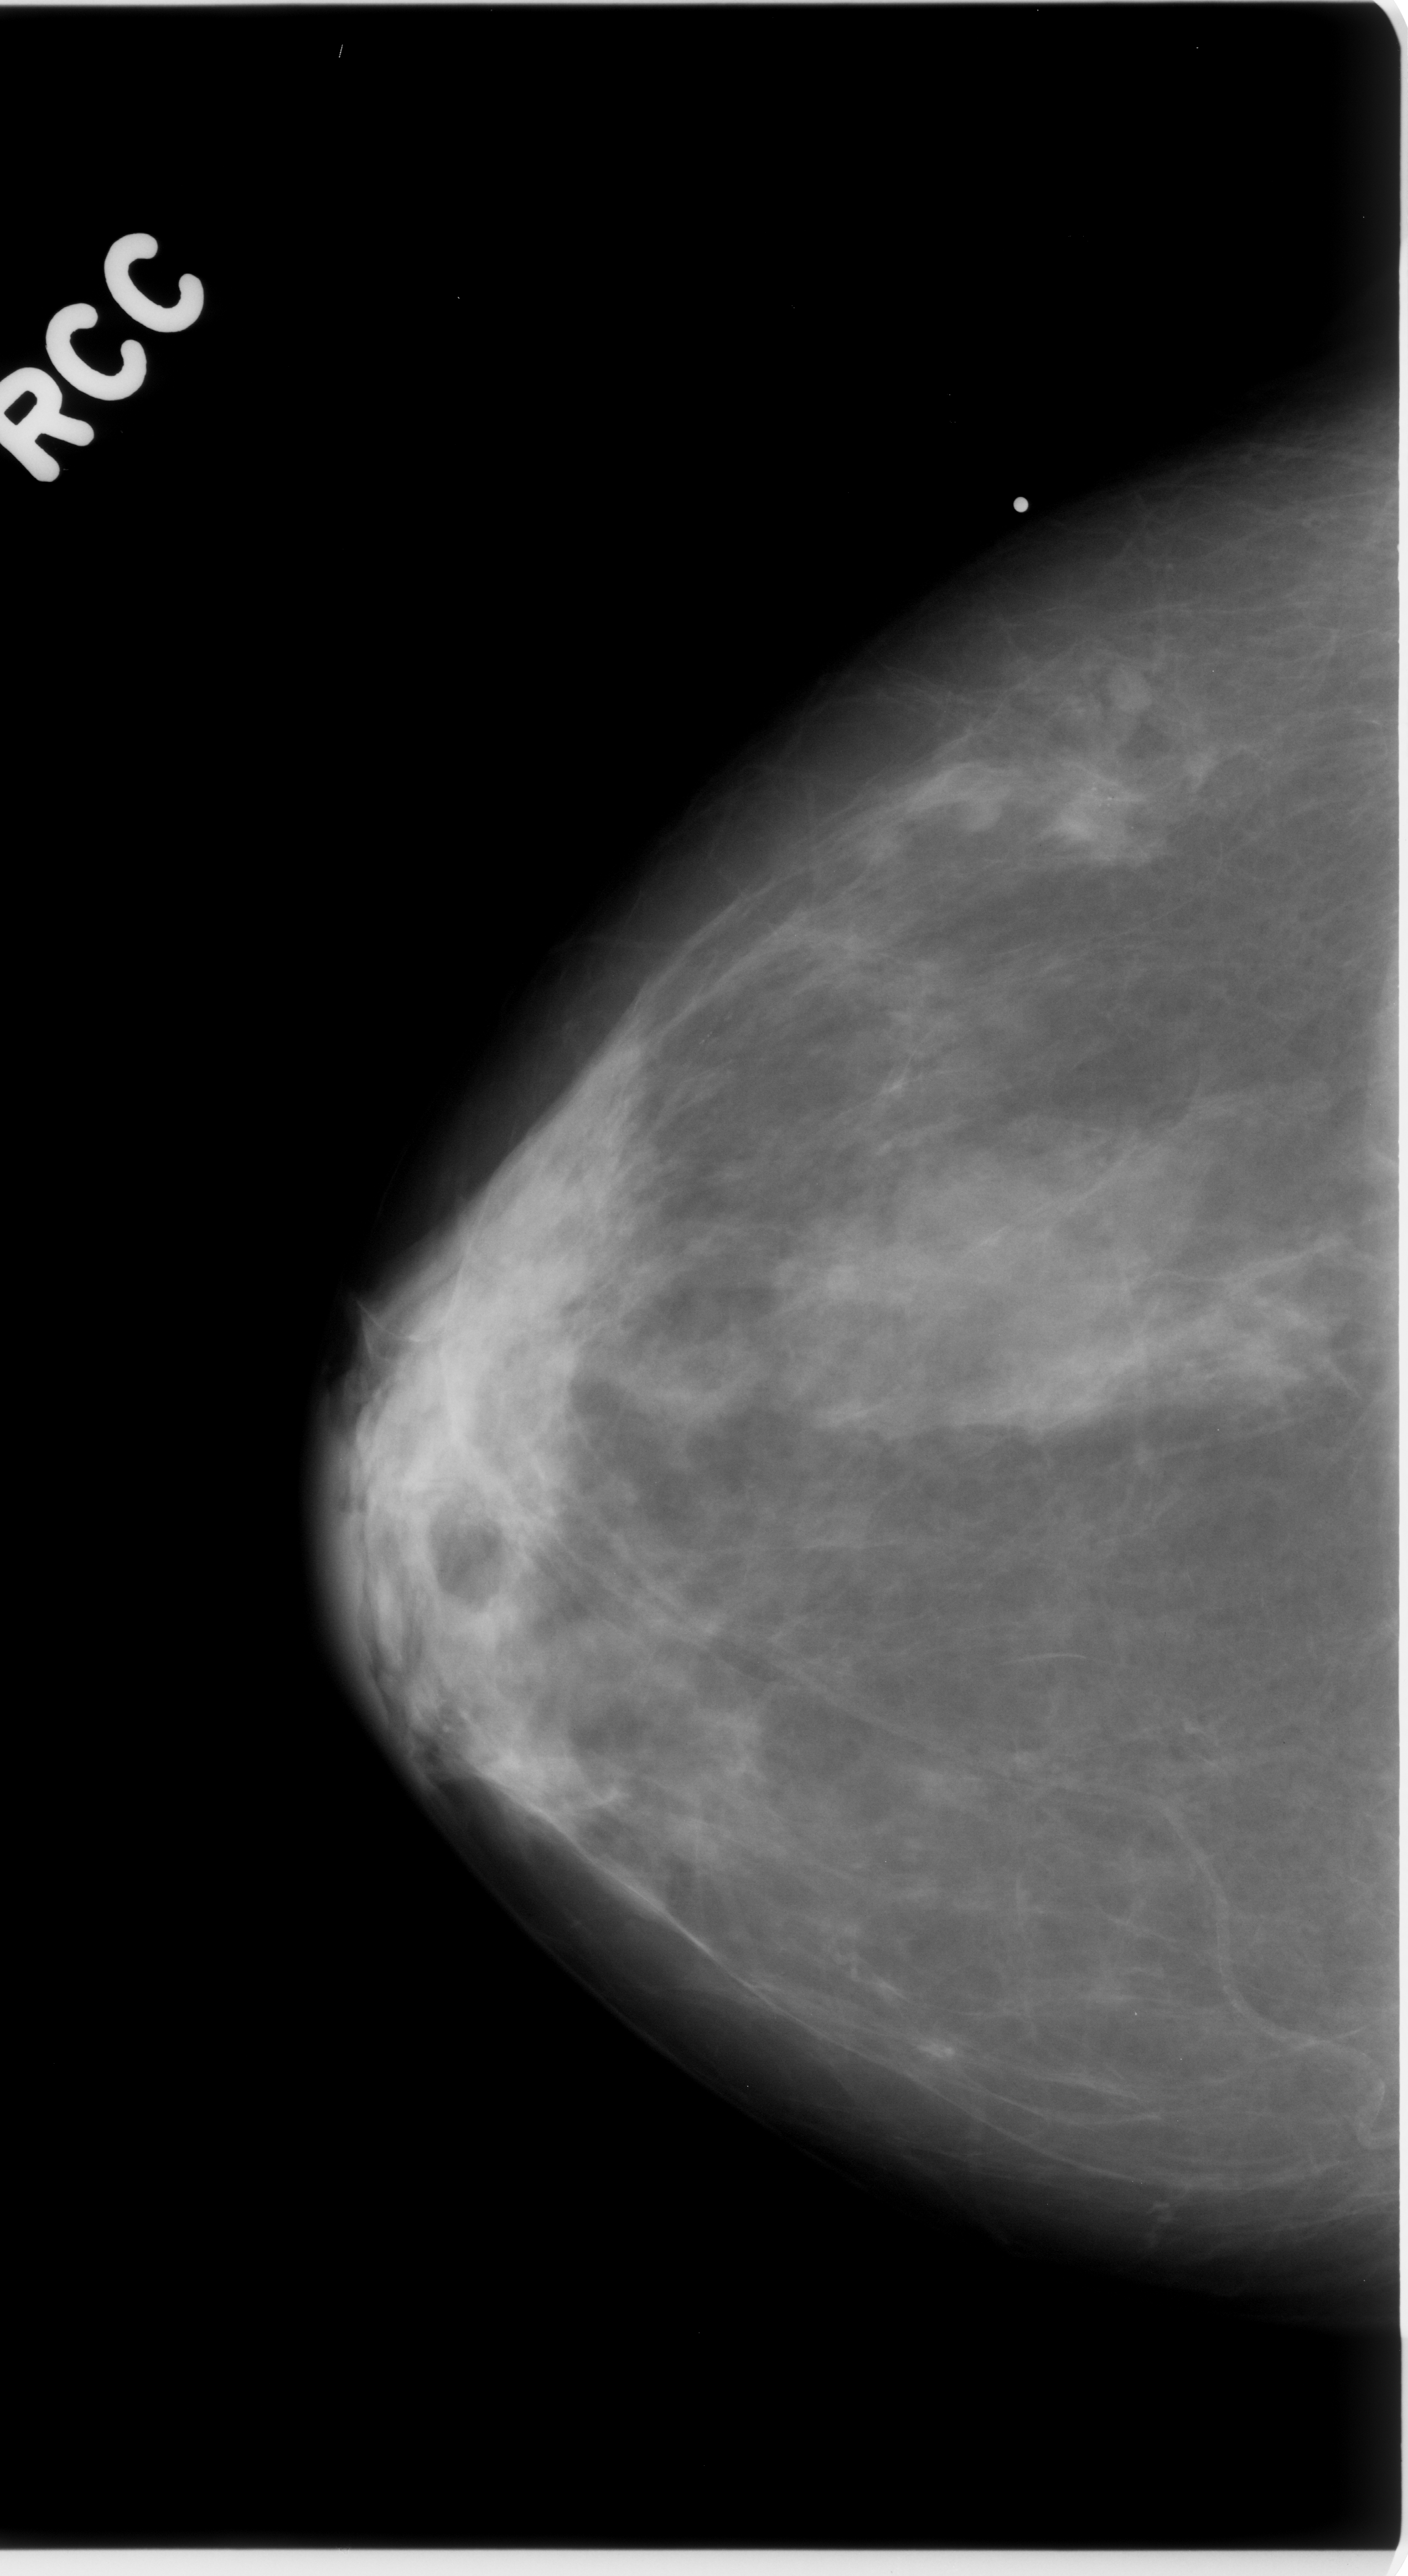
Mammogram (digitized film); right breast; CC view; BI-RADS breast density category 2 (scale 1–4); 1408 × 2576 image matrix.
Marked abnormalities (boxes around the expert regions of interest):
- calcifications, morphology pleomorphic, distribution clustered; BI-RADS assessment category 5; pathology result (as recorded, not read from the image): malignant: box from (x=934, y=668) to (x=1254, y=931) px